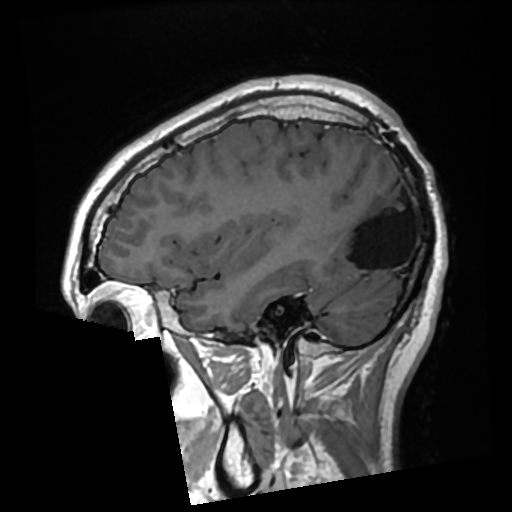
Brain MRI from a brain-tumour surgery series, one sagittal slice; slice 87 of 276 in the series (ordered by position); T1-weighted post-contrast; 0.7 mm slice thickness; 512 × 512 image matrix, field of view 250 × 250 mm. From the clinical record (not read from this slice): histopathology: Glioma with ependymal features; WHO grade: 2; tumour location: Left Parietal.
Annotated regions visible in this slice (outlined manually by an expert reader):
- previous resection cavity: box from (x=338, y=182) to (x=410, y=268) px